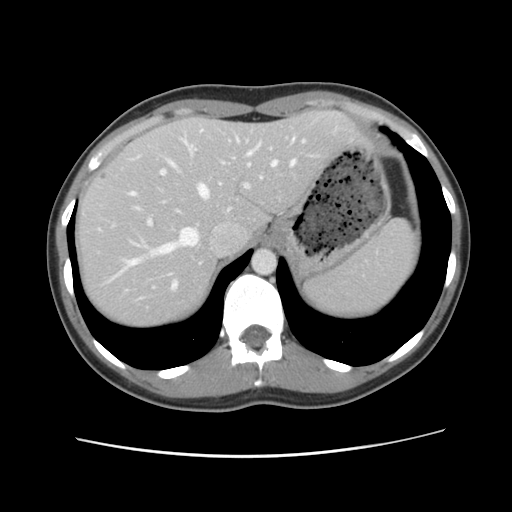
Contrast-enhanced abdominal CT, one axial slice; slice 90 of 134 in the series (ordered by position); 120 kVp; intravenous contrast given; soft-tissue window (W 400 / L 40 HU); 512 × 512 image matrix, field of view 339 × 339 mm. Female patient, age 33 years. Case-level facts recorded for this patient, not image findings: diagnosis: colorectal cancer liver metastases, imaged before liver resection.
Annotated regions visible in this slice (outlined manually by an expert reader):
- hepatic veins: bounding box [x1, y1, x2, y2] px = [116, 130, 305, 290]
- liver: [76, 112, 363, 328]
- planned liver remnant (the part of the liver to remain after resection): [75, 112, 363, 329]
- portal vein (with intrahepatic branches): [132, 139, 273, 227]
- liver metastasis: [99, 172, 108, 181]